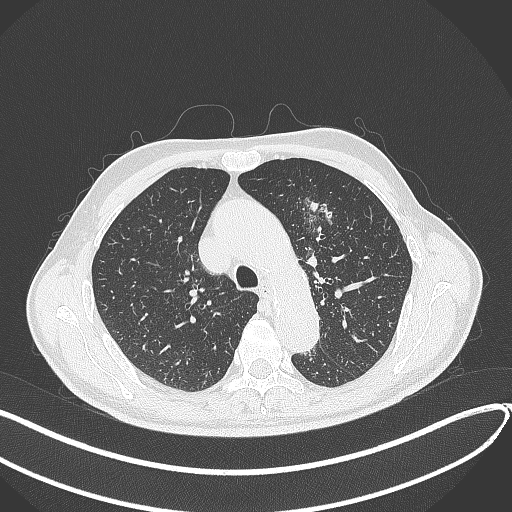
Chest CT, one axial slice. Position 298 of 459 along the scan axis. Reconstruction kernel B70f. Lung window (W 1500 / L -600 HU). 1 mm slice thickness. 512 × 512 image matrix, field of view 400 × 400 mm. Patient: male, 74 years. From the clinical record (not read from this slice): clinical TNM (as recorded): T2b N0 M1c.
Outlined on this slice (rectangle marked by the reading radiologist):
- lung tumour (recorded histology: adenocarcinoma): bounding box (x1, y1, x2, y2) in pixels: (303, 189, 347, 248)